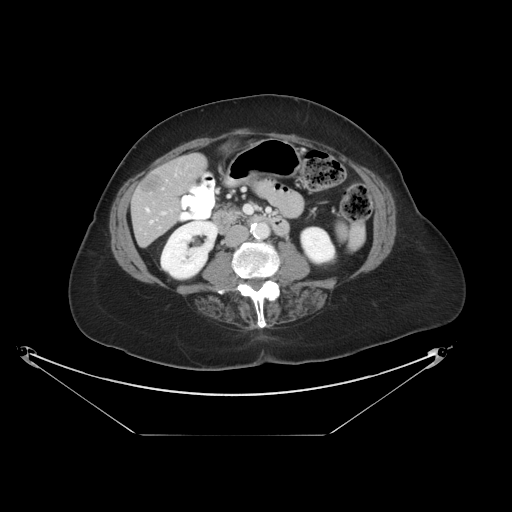
Contrast-enhanced abdominal CT, one axial slice; reconstruction kernel STANDARD; intravenous contrast given; soft-tissue window (W 400 / L 40 HU); 5 mm slice thickness; 512 × 512 image matrix. Female patient, age 70 years. From the clinical record (not read from this slice): diagnosis: colorectal cancer liver metastases, imaged before liver resection; multiple liver metastases: no; largest metastasis: 2.5 cm; disease in both lobes: no.
Outlined on this slice (manually delineated by an expert):
- hepatic veins: bounding box <146,208,153,223> (left, top, right, bottom; pixels)
- liver: <133,155,205,246>
- planned liver remnant (the part of the liver to remain after resection): <156,155,206,231>
- liver metastasis: <141,173,164,194>